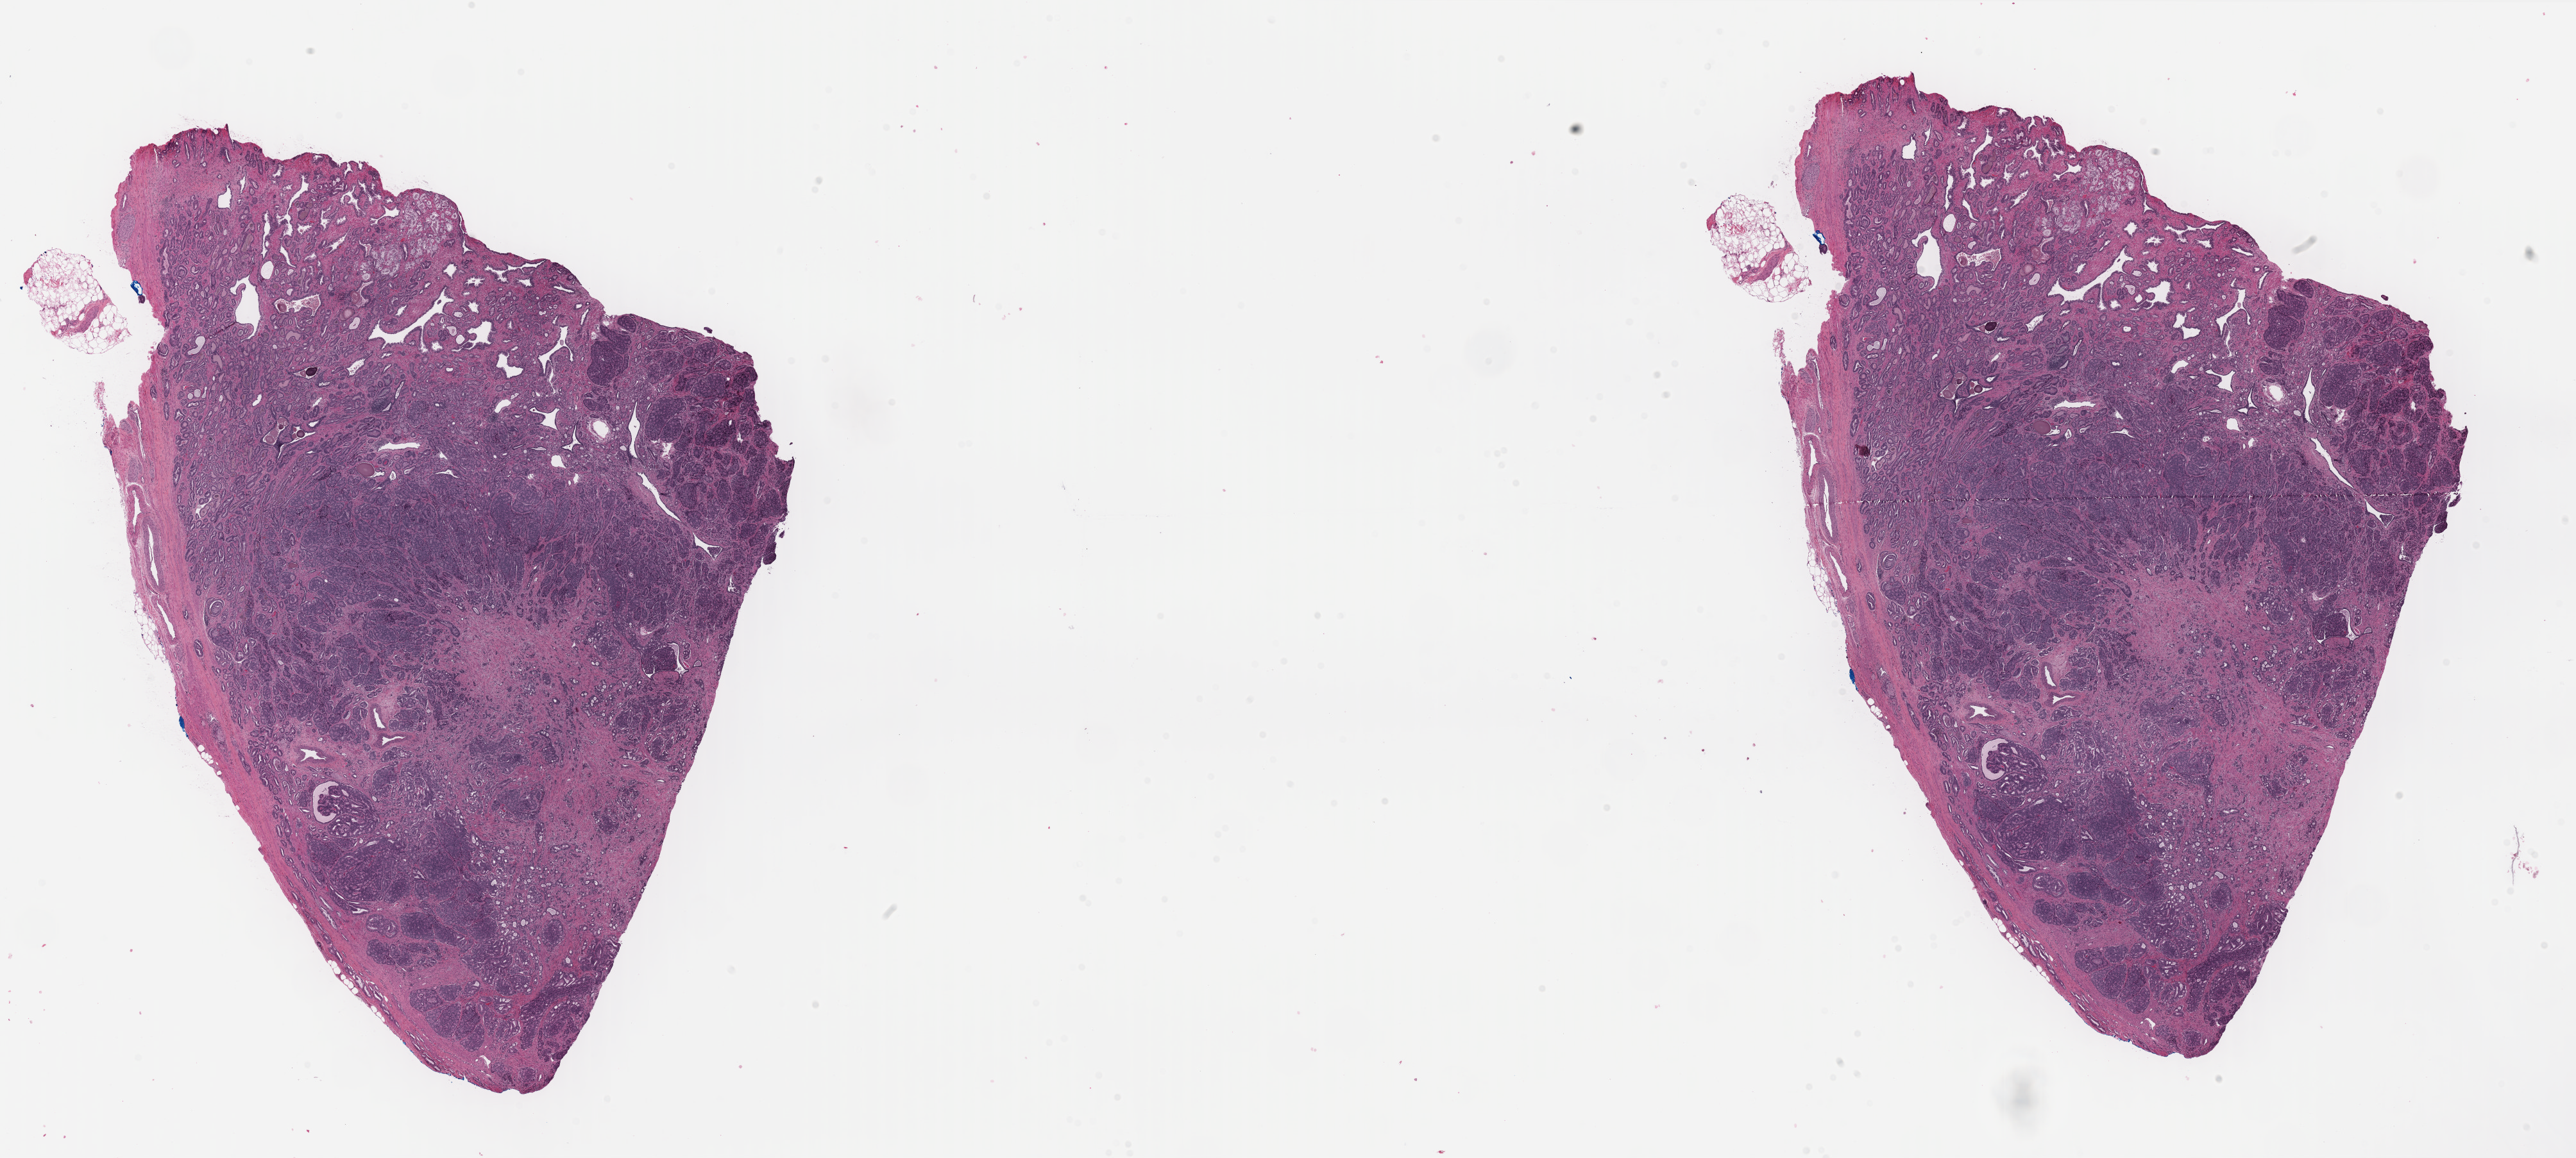
H&E whole-slide image — low-resolution overview of the scanned area, about 31.8 x 14.3 mm (acquisition: 40x scan), FFPE section, prostate, primary tumour sample. Patient: male, age at initial diagnosis 62 years. Gleason score: 7 (4+3).
Diagnosis: Adenocarcinoma, NOS. Lymph nodes positive (case pathology): 0 of 9 examined.